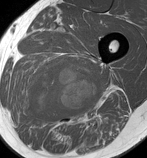
MRI of an extremity soft-tissue mass, one axial slice. Position 75 of 86 along the scan axis. MR volume resampled by the dataset authors to the PET/CT grid (not the native acquisition matrix). 147 × 158 image matrix, field of view 144 × 154 mm. Male patient. Case-level facts recorded for this patient, not image findings: histological type: undifferentiated pleomorphic liposarcoma; grade: high; site of the primary tumour: left thigh.
Outlined on this slice (expert contour drawn on MRI and transferred to this co-registered scan by the dataset authors):
- gross tumour volume including surrounding oedema: bounding box (x1, y1, x2, y2) in pixels: (21, 62, 108, 125)
- gross tumour volume (mass): (28, 63, 100, 121)